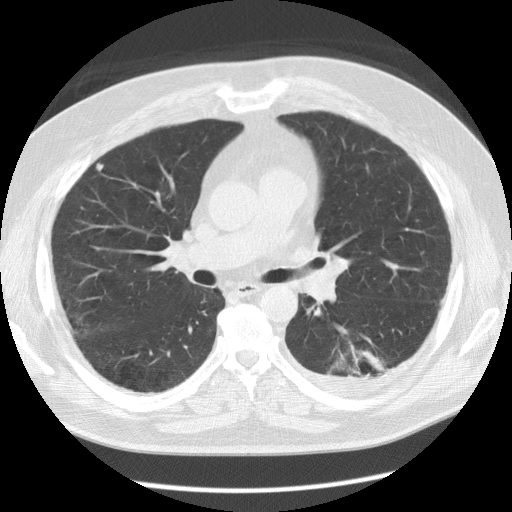
Low-dose screening chest CT, one axial slice; position 74 of 126 along the scan axis; lung window (W 1500 / L -600 HU); 2.5 mm slice thickness; 512 × 512 image matrix, field of view 370 × 370 mm.
Structures marked on this image (outlined manually by an expert reader):
- lesion 1 (tumor, lower lobe of left lung): bounding box (x1, y1, x2, y2) in pixels: (358, 351, 385, 371)